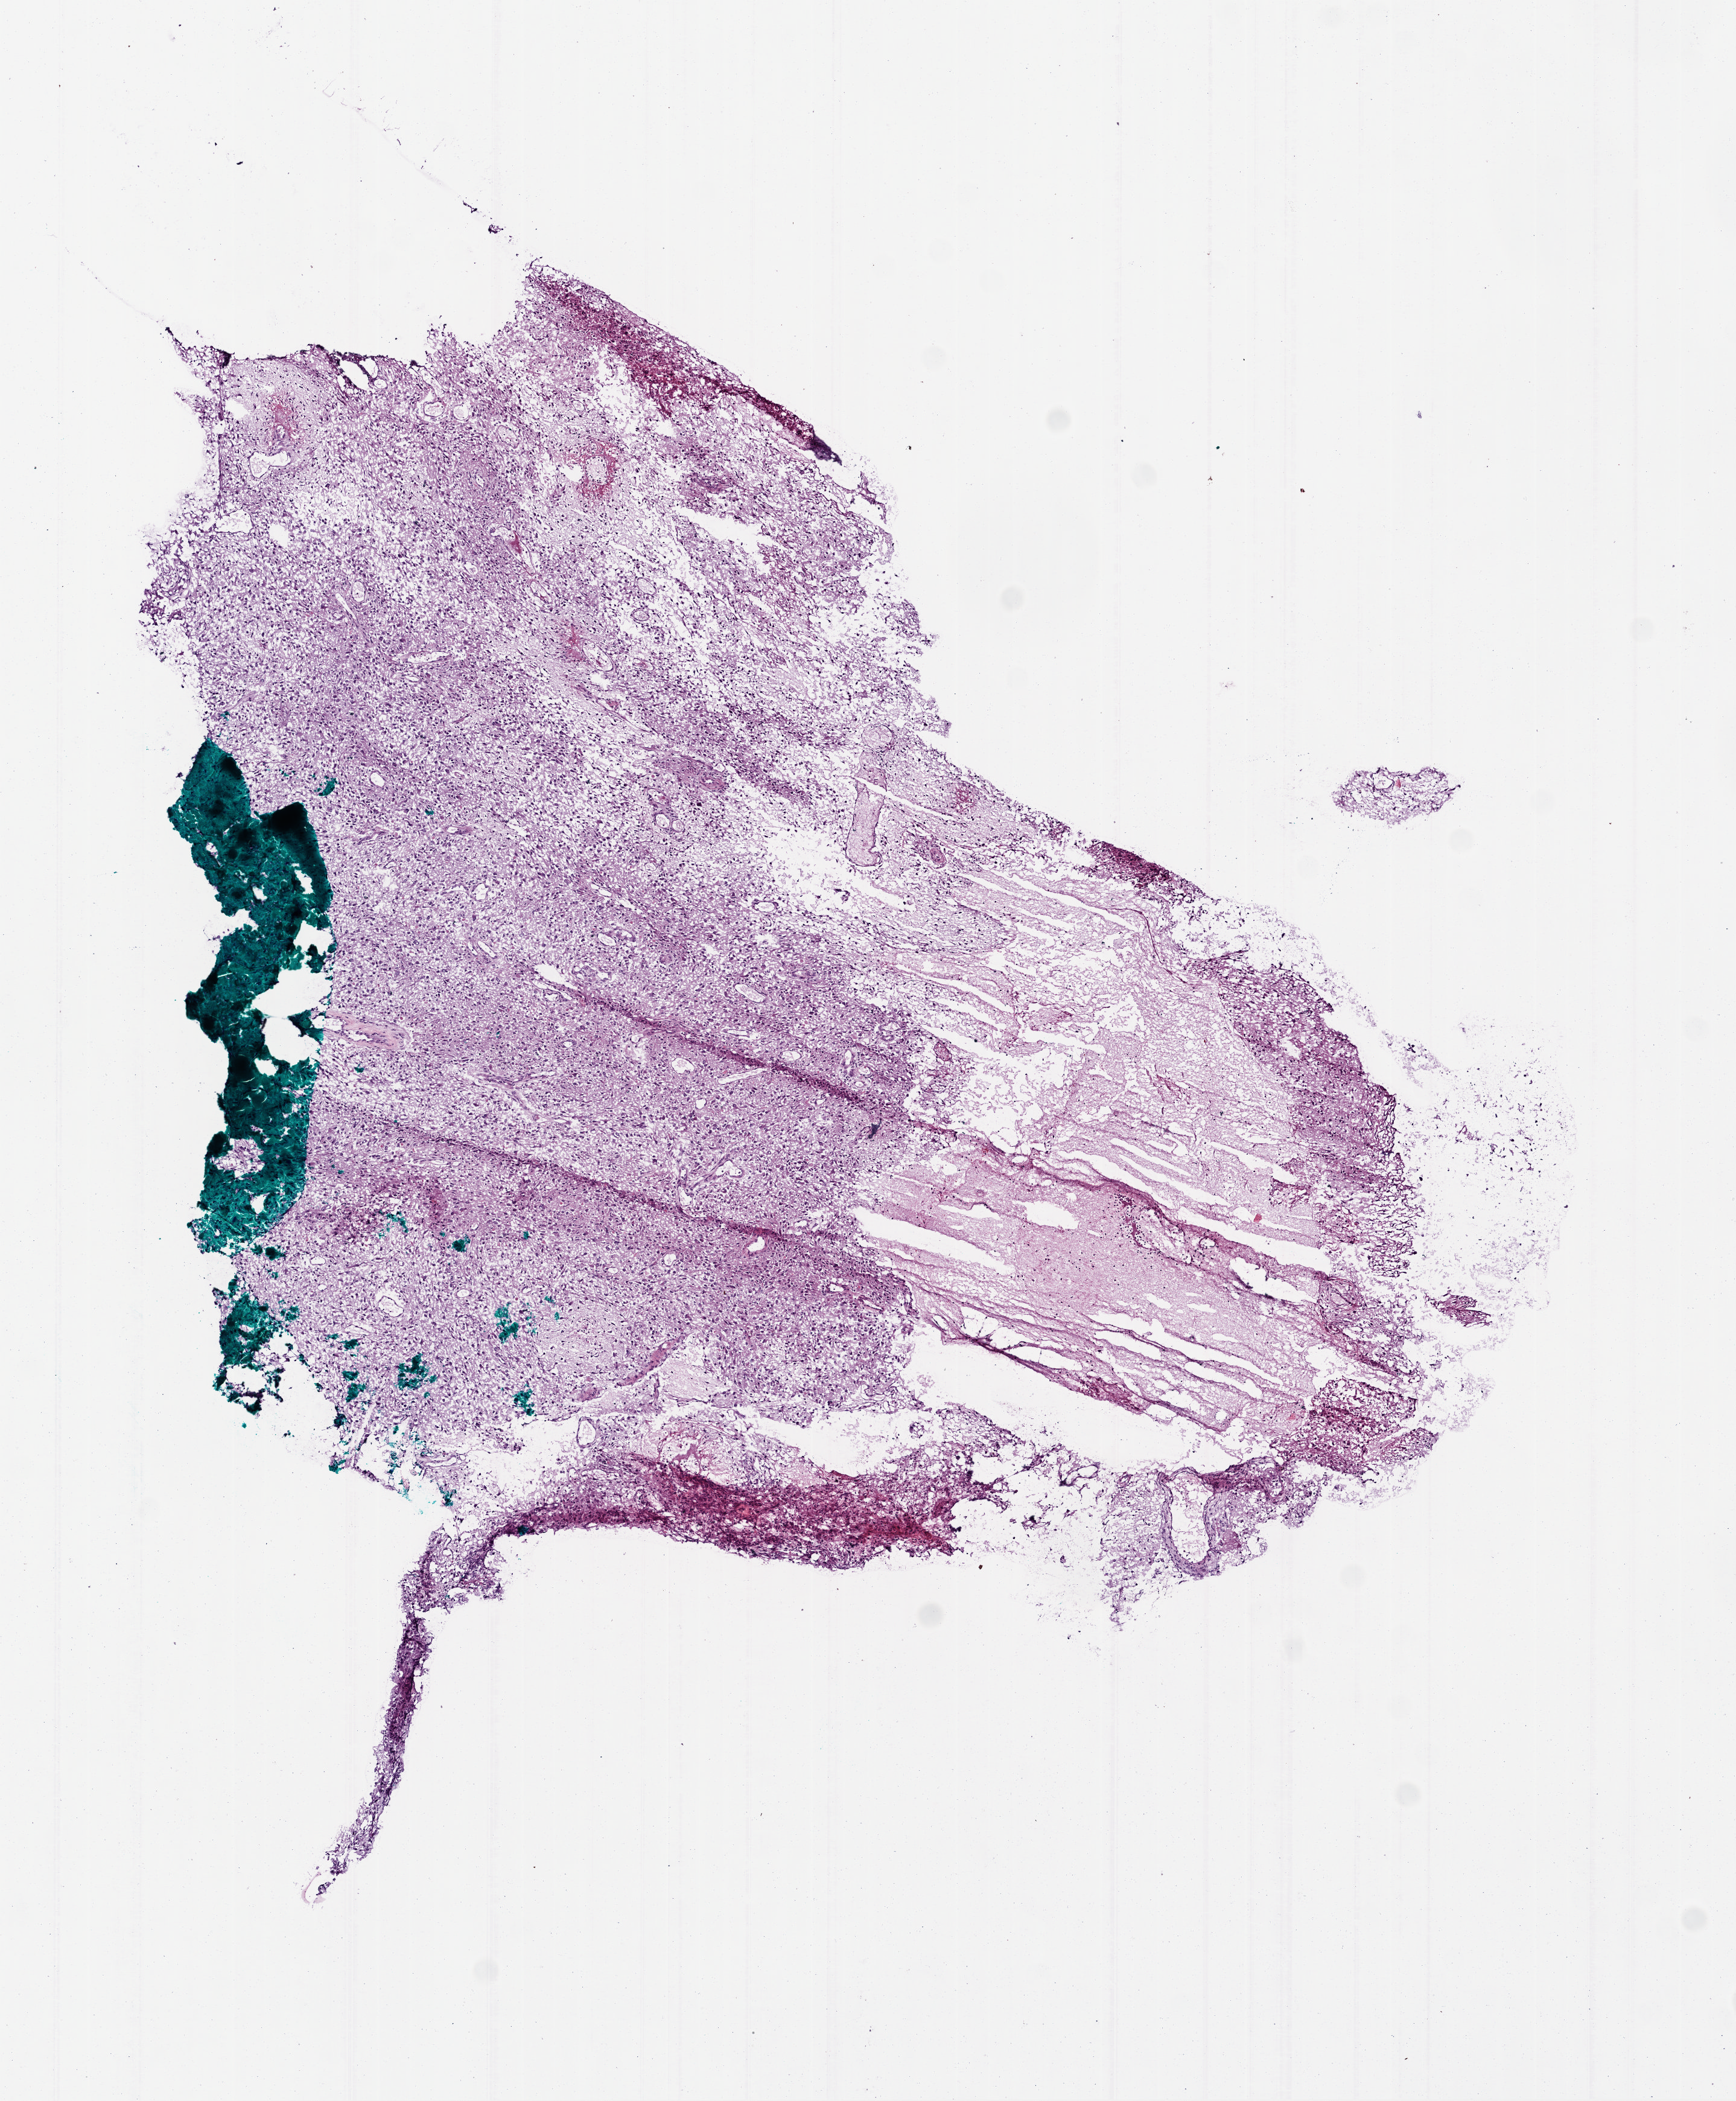
Digitized H&E-stained tissue section (whole slide), whole scanned area (about 5.8 x 7.0 mm, slide scanned at 20x) shown as a low-resolution overview. Frozen section from the bottom of the tissue portion. Brain, primary tumour sample. Patient: male, age at initial diagnosis 43 years. Pathologist review of this section (percent, as recorded): tumour cells 85%, tumour nuclei 85%, normal cells 5%, stromal cells 5%, necrosis 5%.
- histologic diagnosis: Glioblastoma